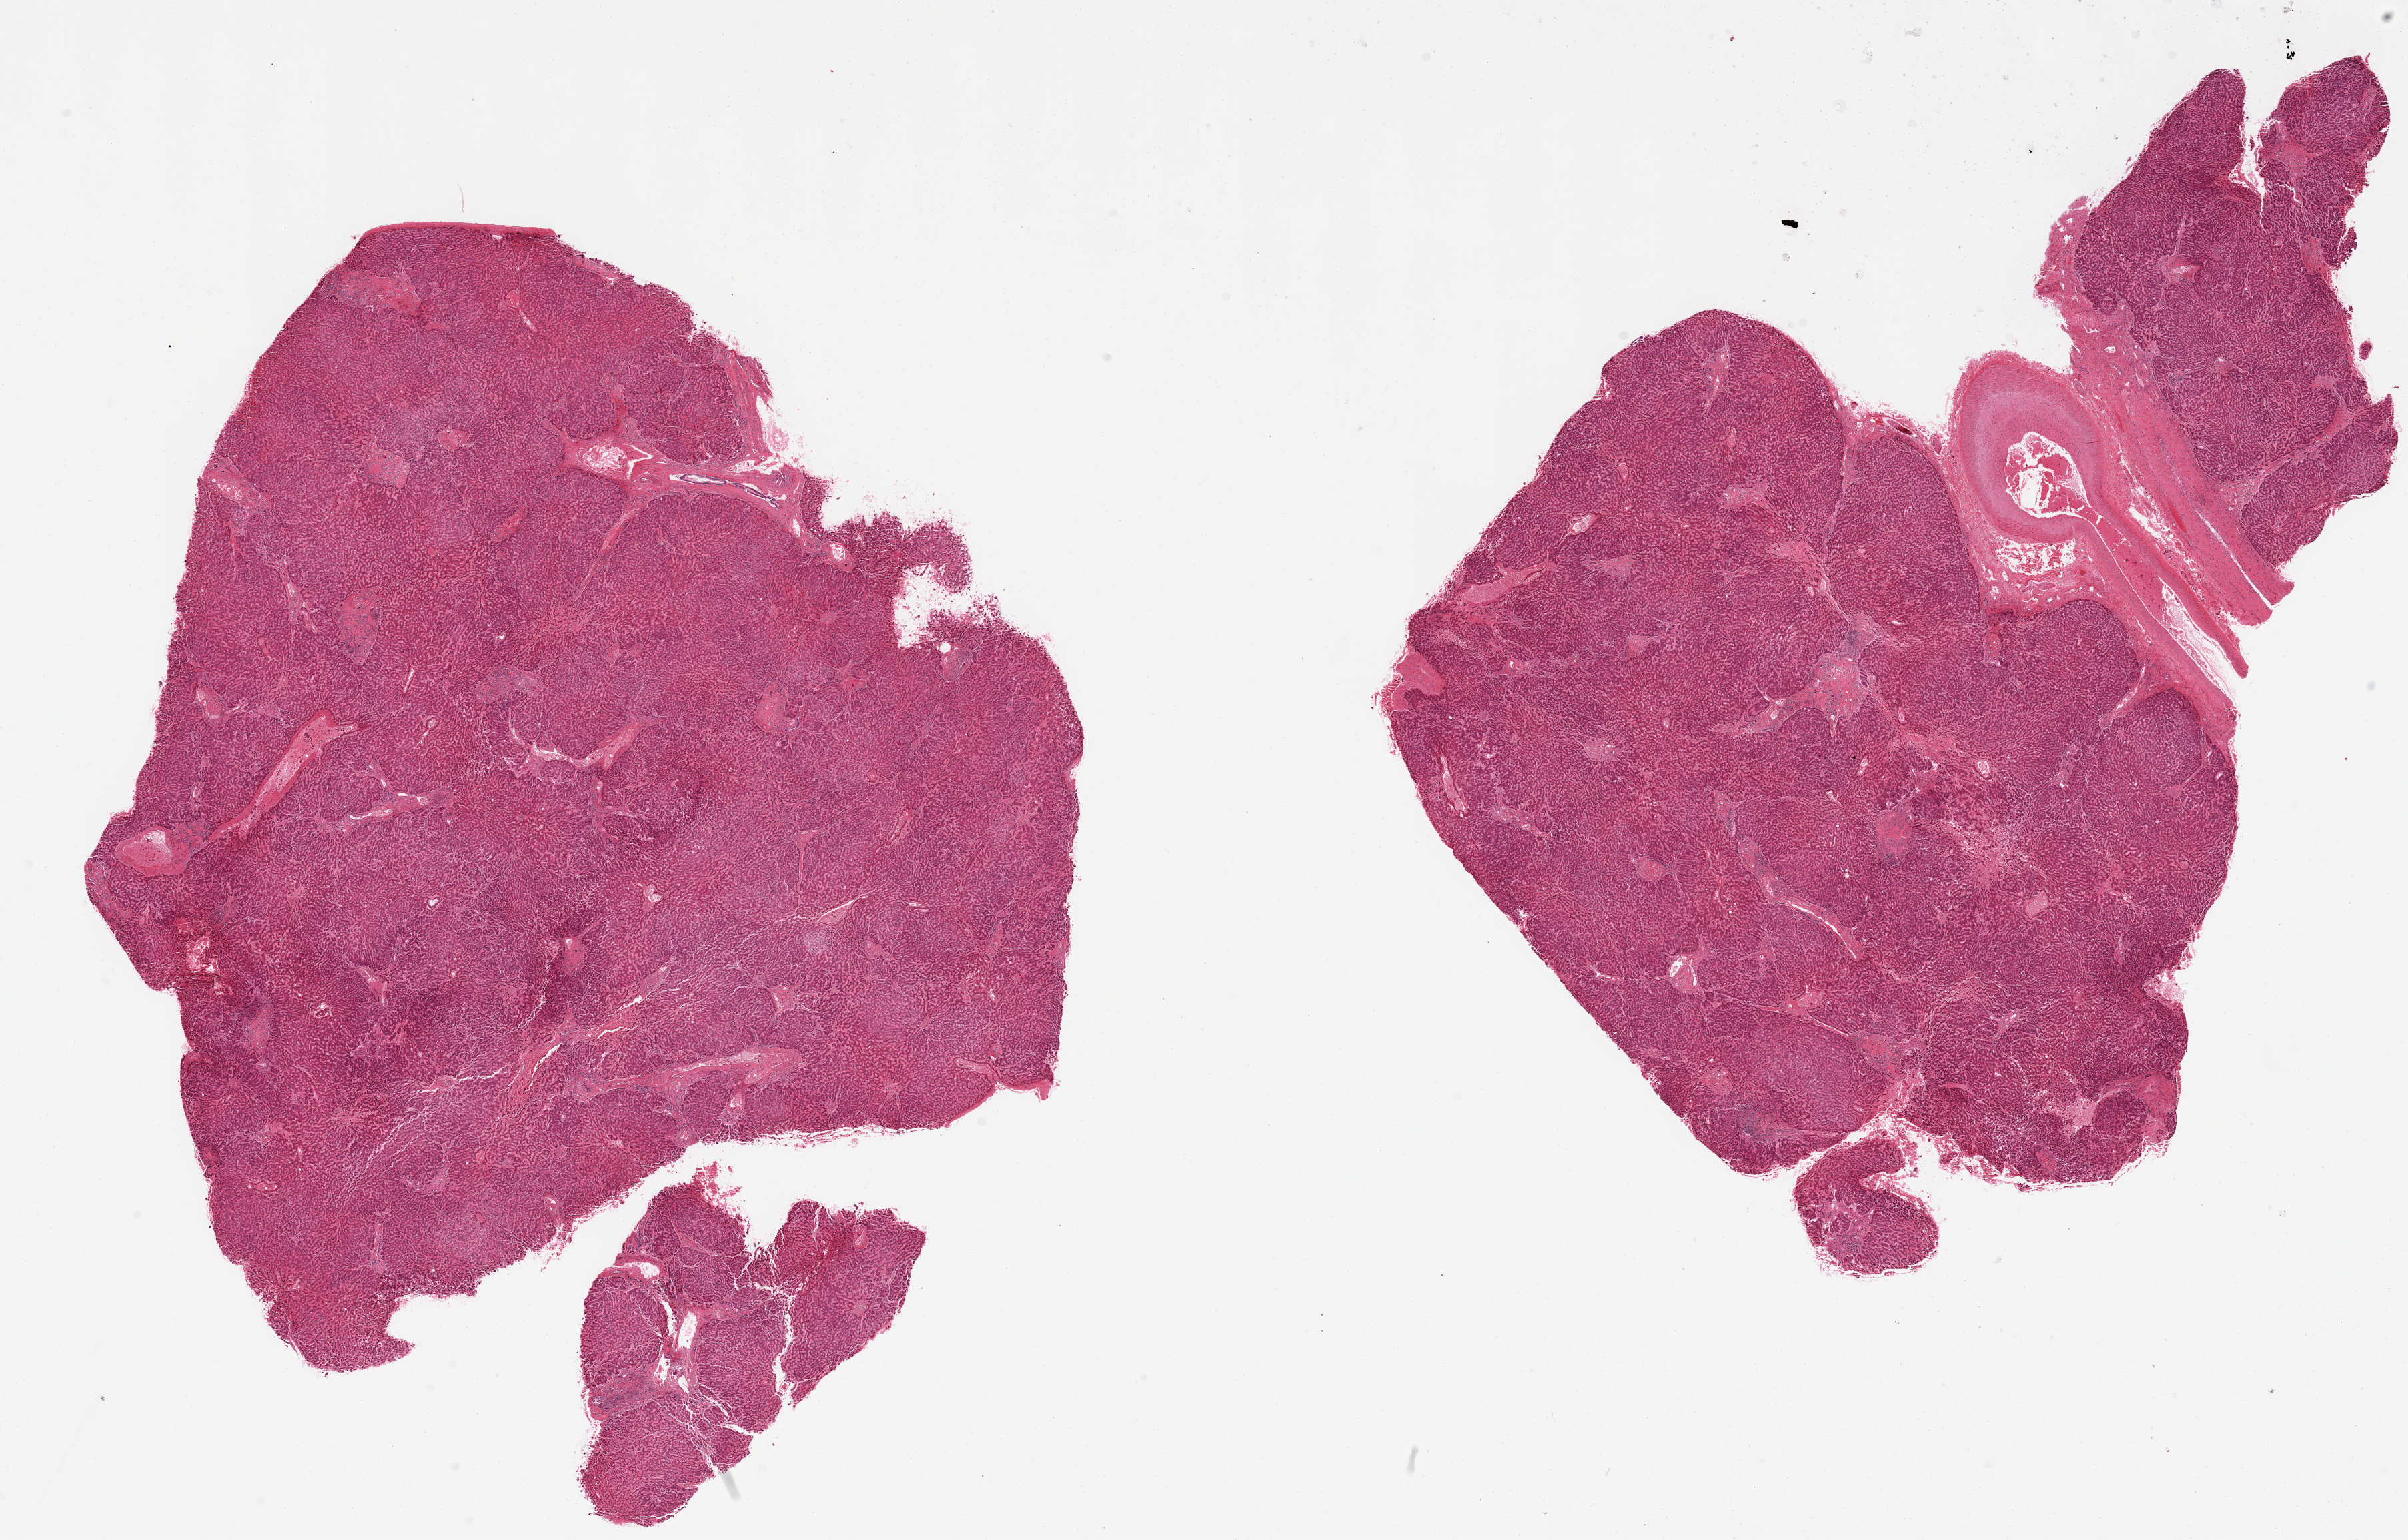
Whole-slide image, H&E stain, brightfield — shown as a low-resolution overview of the whole scanned area (about 28.5 x 18.3 mm); PAXgene-fixed paraffin-embedded (PFPE) section; target tissue: liver; donor tissue sample. Donor: male.
* review note (as recorded): 2 pieces; chronic inflammation and fibrosis